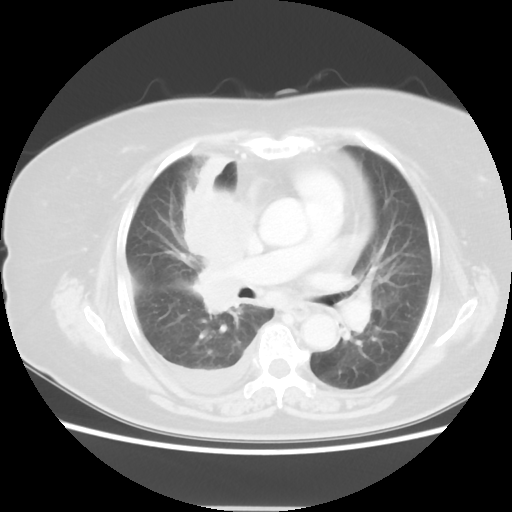
Chest CT, one axial slice; reconstruction kernel STANDARD; 120 kVp; lung window (W 1500 / L -600 HU); 5 mm slice thickness; 512 × 512 image matrix, field of view 360 × 360 mm. Patient: female, 73 years. From the clinical record (not read from this slice): clinical TNM (as recorded): T3 N3 M1b; histopathological grade: G3.
Outlined on this slice (bounding box drawn by a radiologist):
- lung tumour (recorded histology: small cell carcinoma): box from (x=175, y=148) to (x=263, y=316) px